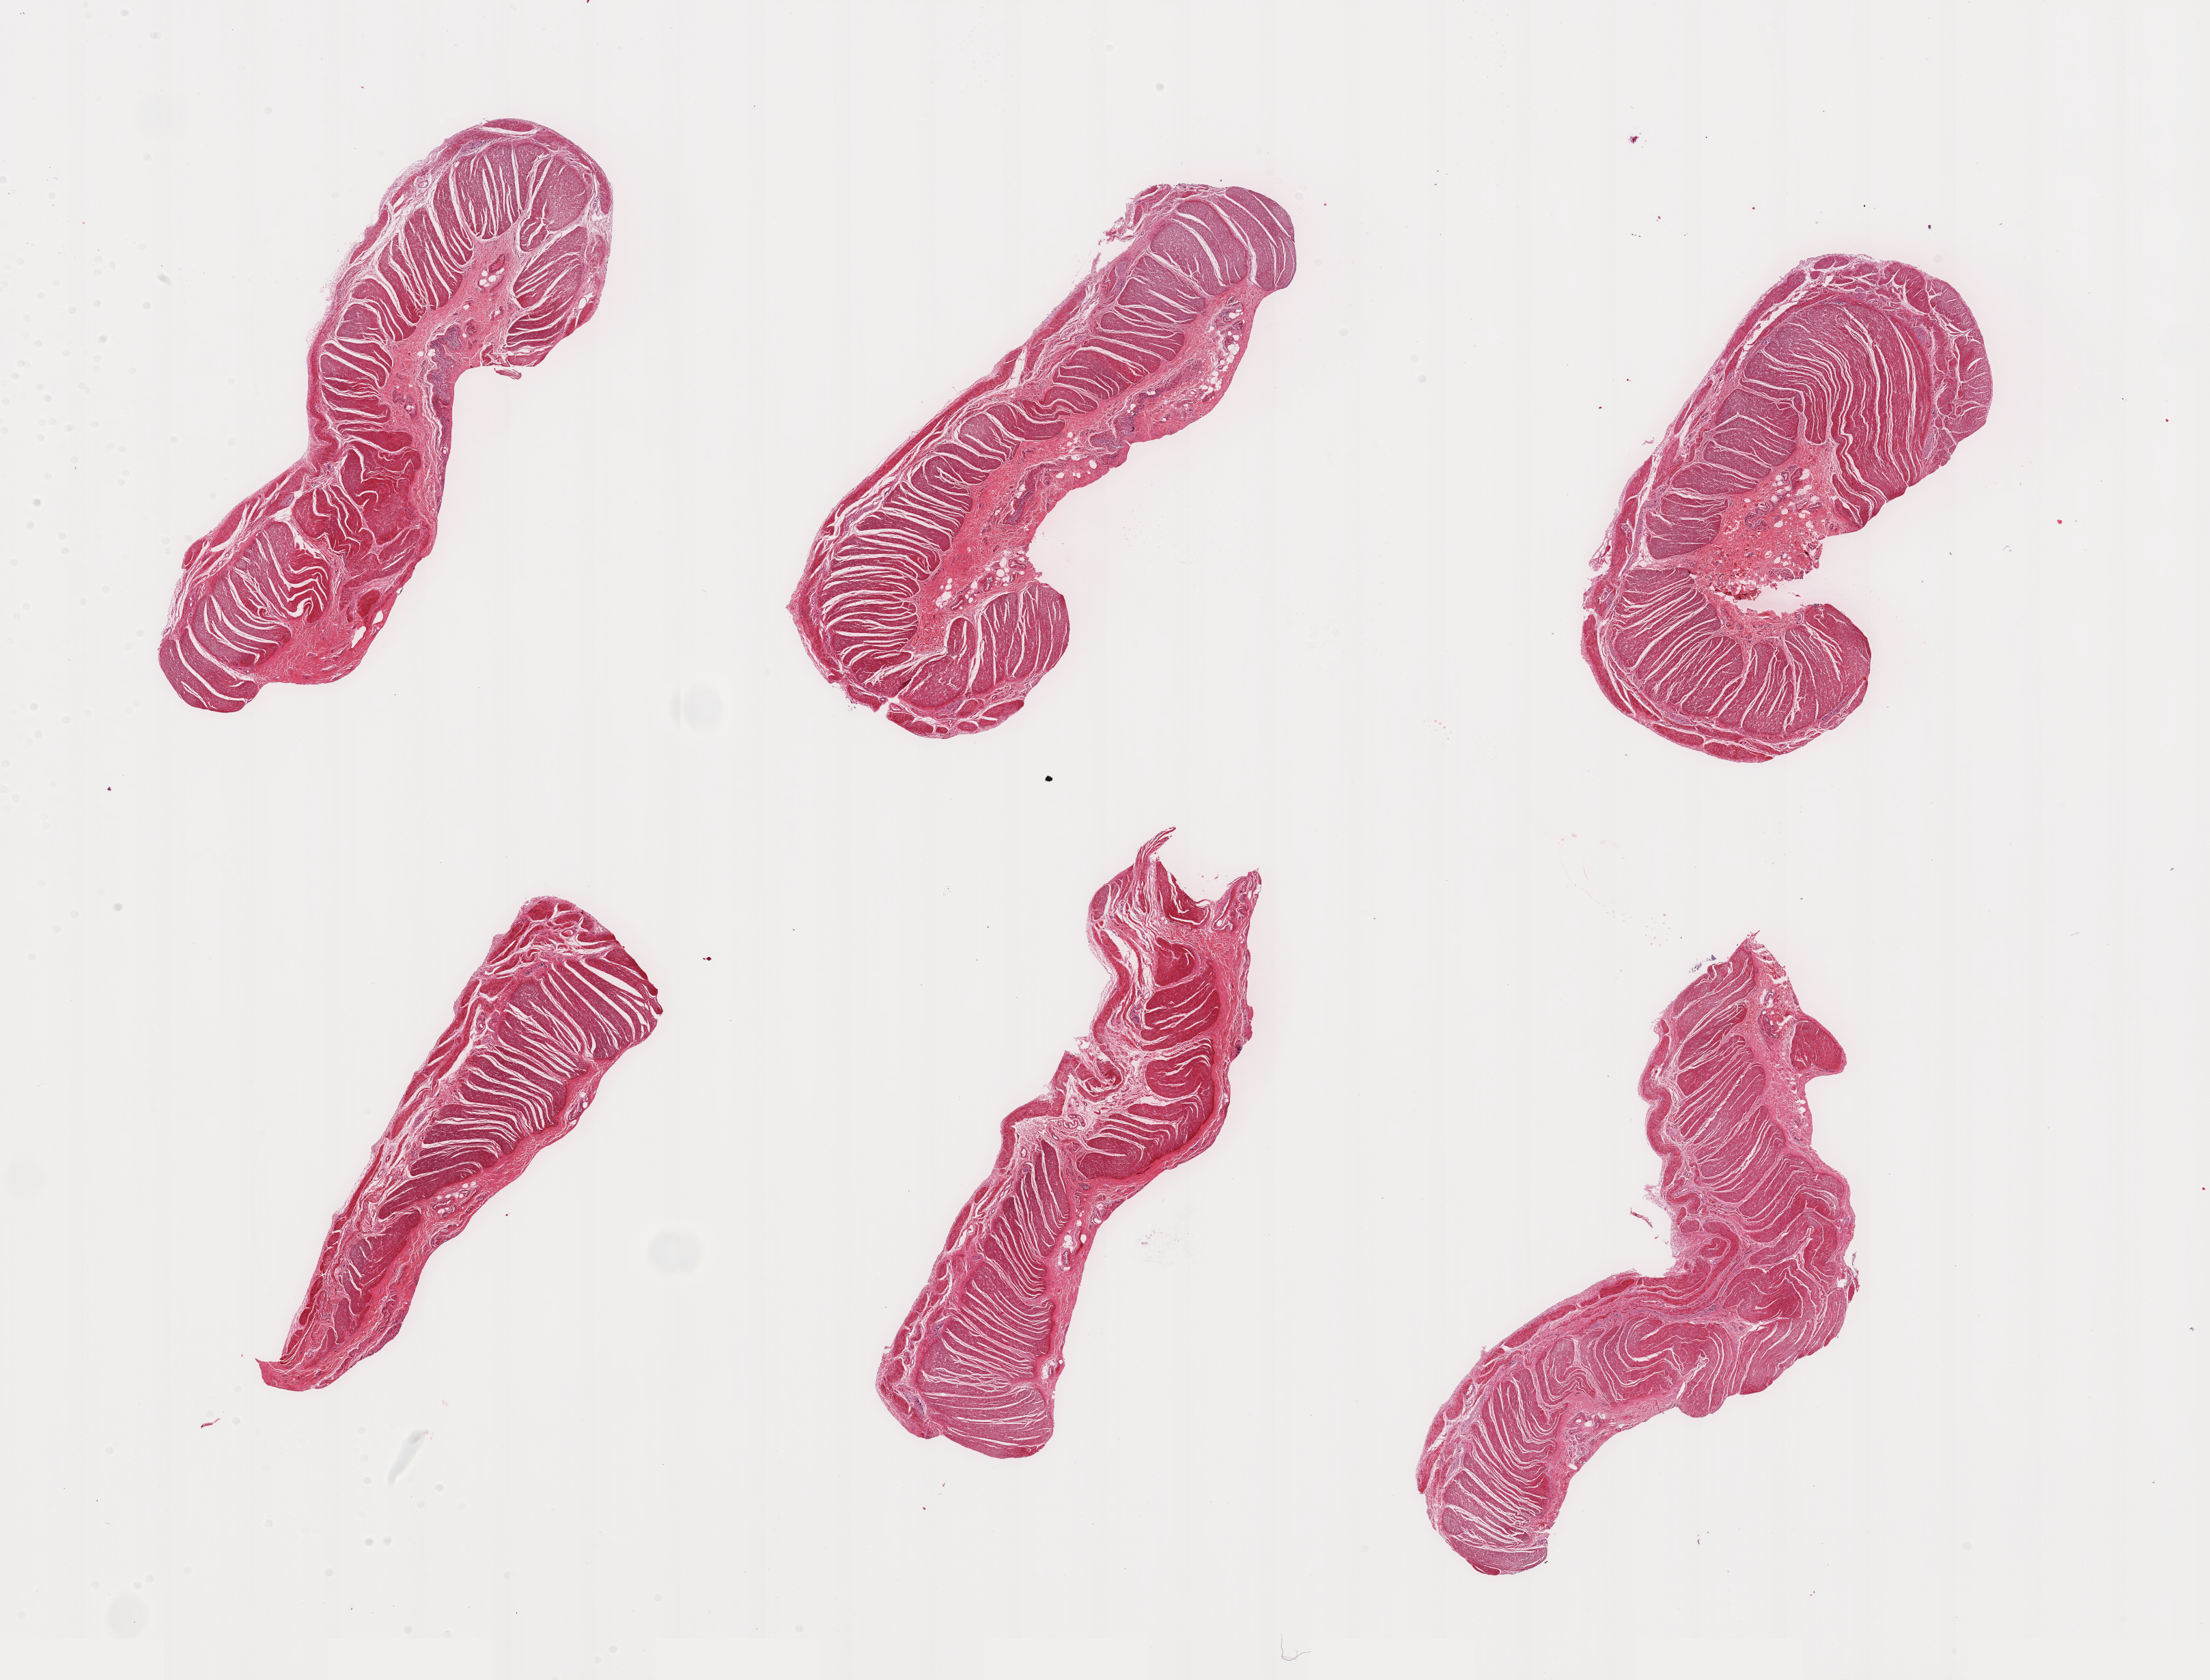
Whole-slide image, hematoxylin and eosin (H&E) stain, brightfield — whole scanned area (about 25.6 x 19.5 mm) shown as a low-resolution overview, PAXgene-fixed paraffin-embedded (PFPE) section, section of sigmoid colon (target tissue), donor tissue sample. Male donor.
Reviewer comment on this tissue sample: 6 pieces; well dissected muscle with variable amounts of fibrofatty submucosa.